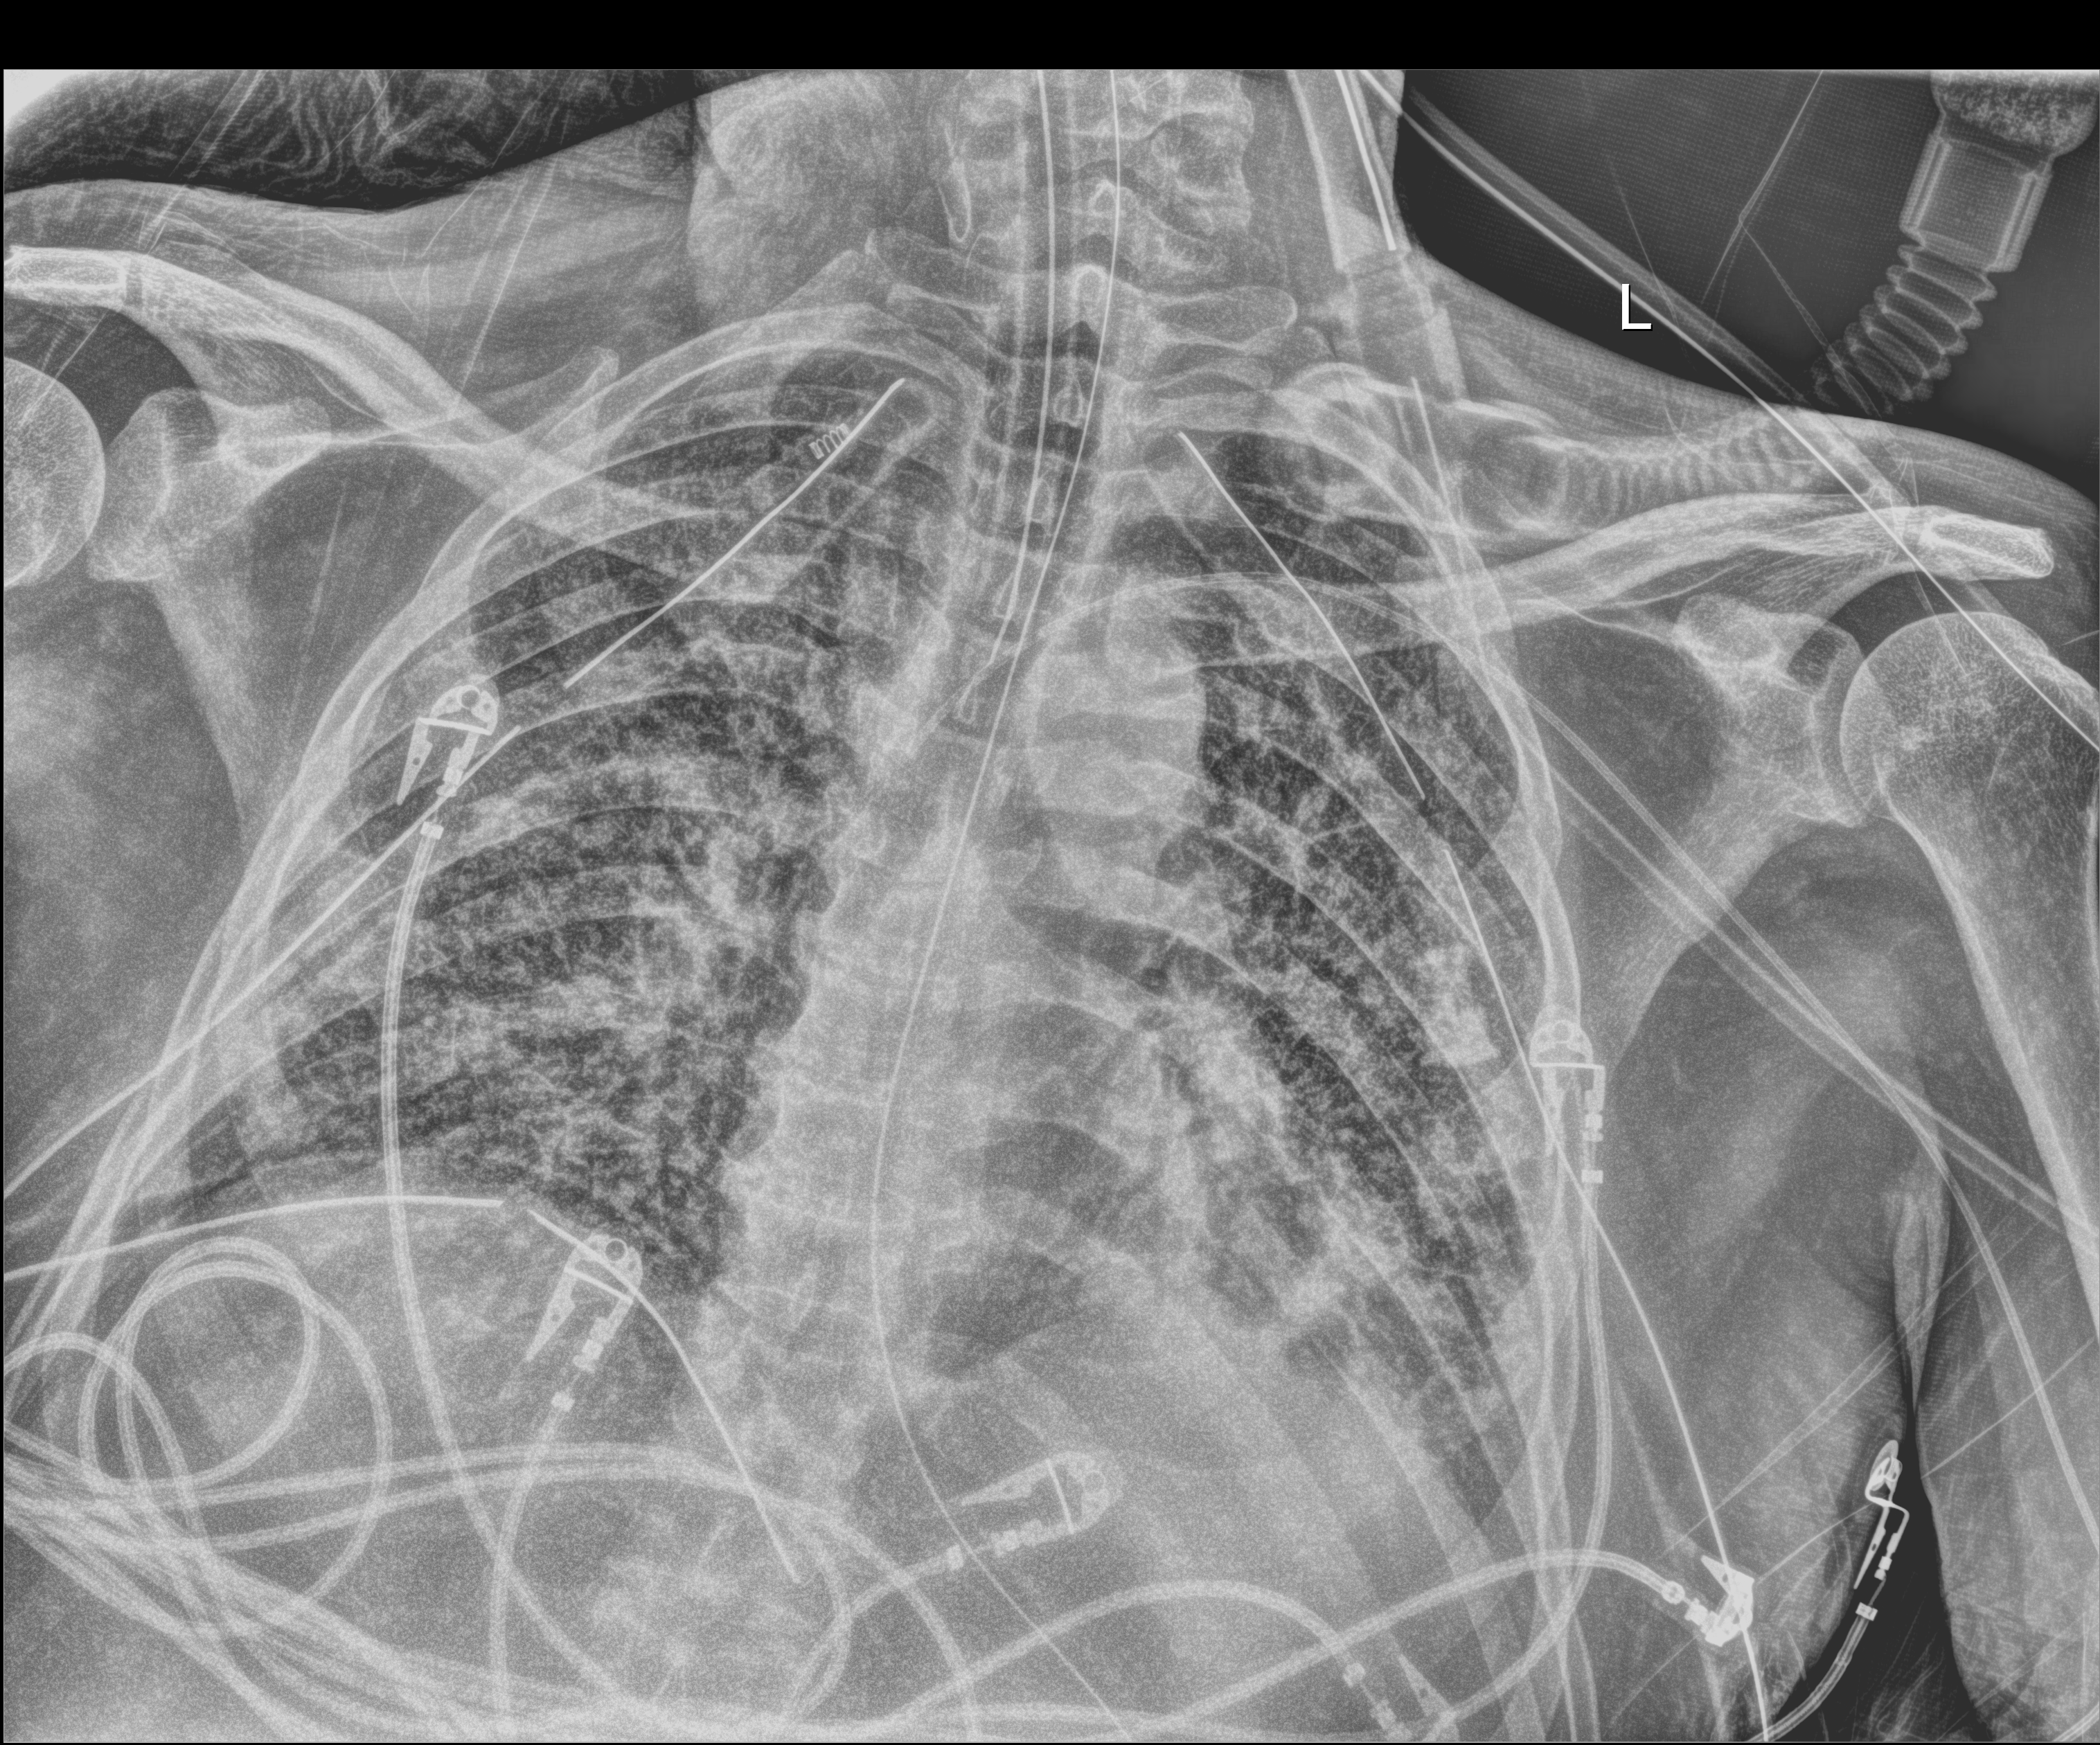
Portable chest radiograph, anteroposterior (AP) projection. Male patient hospitalised with COVID-19, age 18–59 years.
Hospital-stay facts (about this admission, not read from this image; timing relative to this image not recorded): mechanically ventilated during this hospital stay: yes; admitted to intensive care during this hospital stay: yes.